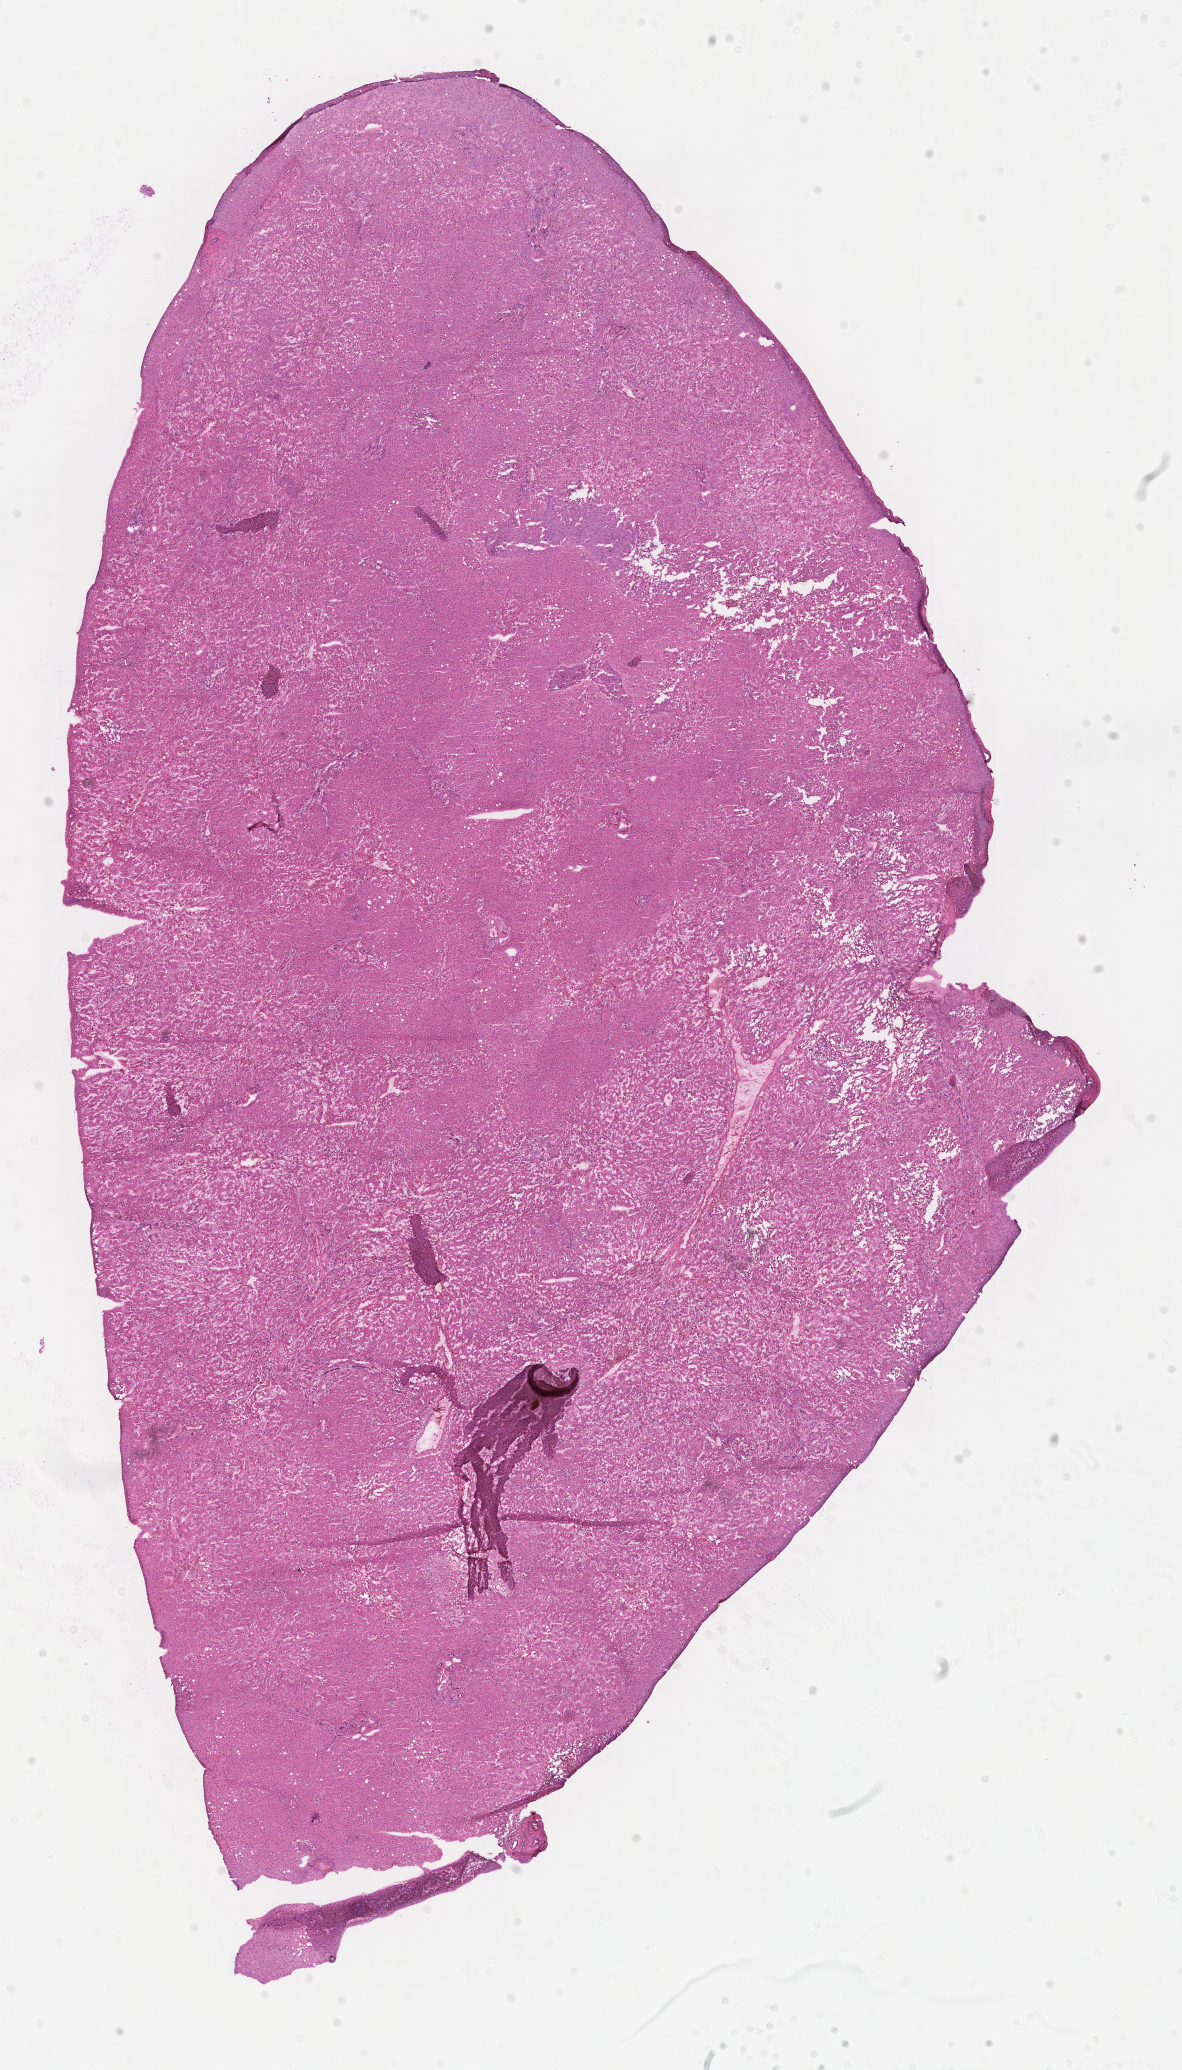
Hematoxylin and eosin (H&E) whole-slide image — whole scanned area (about 9.6 x 16.7 mm) shown as a low-resolution overview, frozen section (tissue freezing medium), normal-tissue sample (non-tumor) from a patient with adenocarcinoma, NOS, anatomic site: rectum. Male patient; age at initial diagnosis 34 years. Pathologist review of this section (percent, as recorded): tumor cells 0%, tumor nuclei 0%, stromal cells 0%, necrosis 0%, normal cells 100%. Infiltration values recorded for this section: lymphocyte infiltration 0%, monocyte infiltration 0%, neutrophil infiltration 0%.
This section: non-tumor tissue sample; the patient's diagnosis is given above.